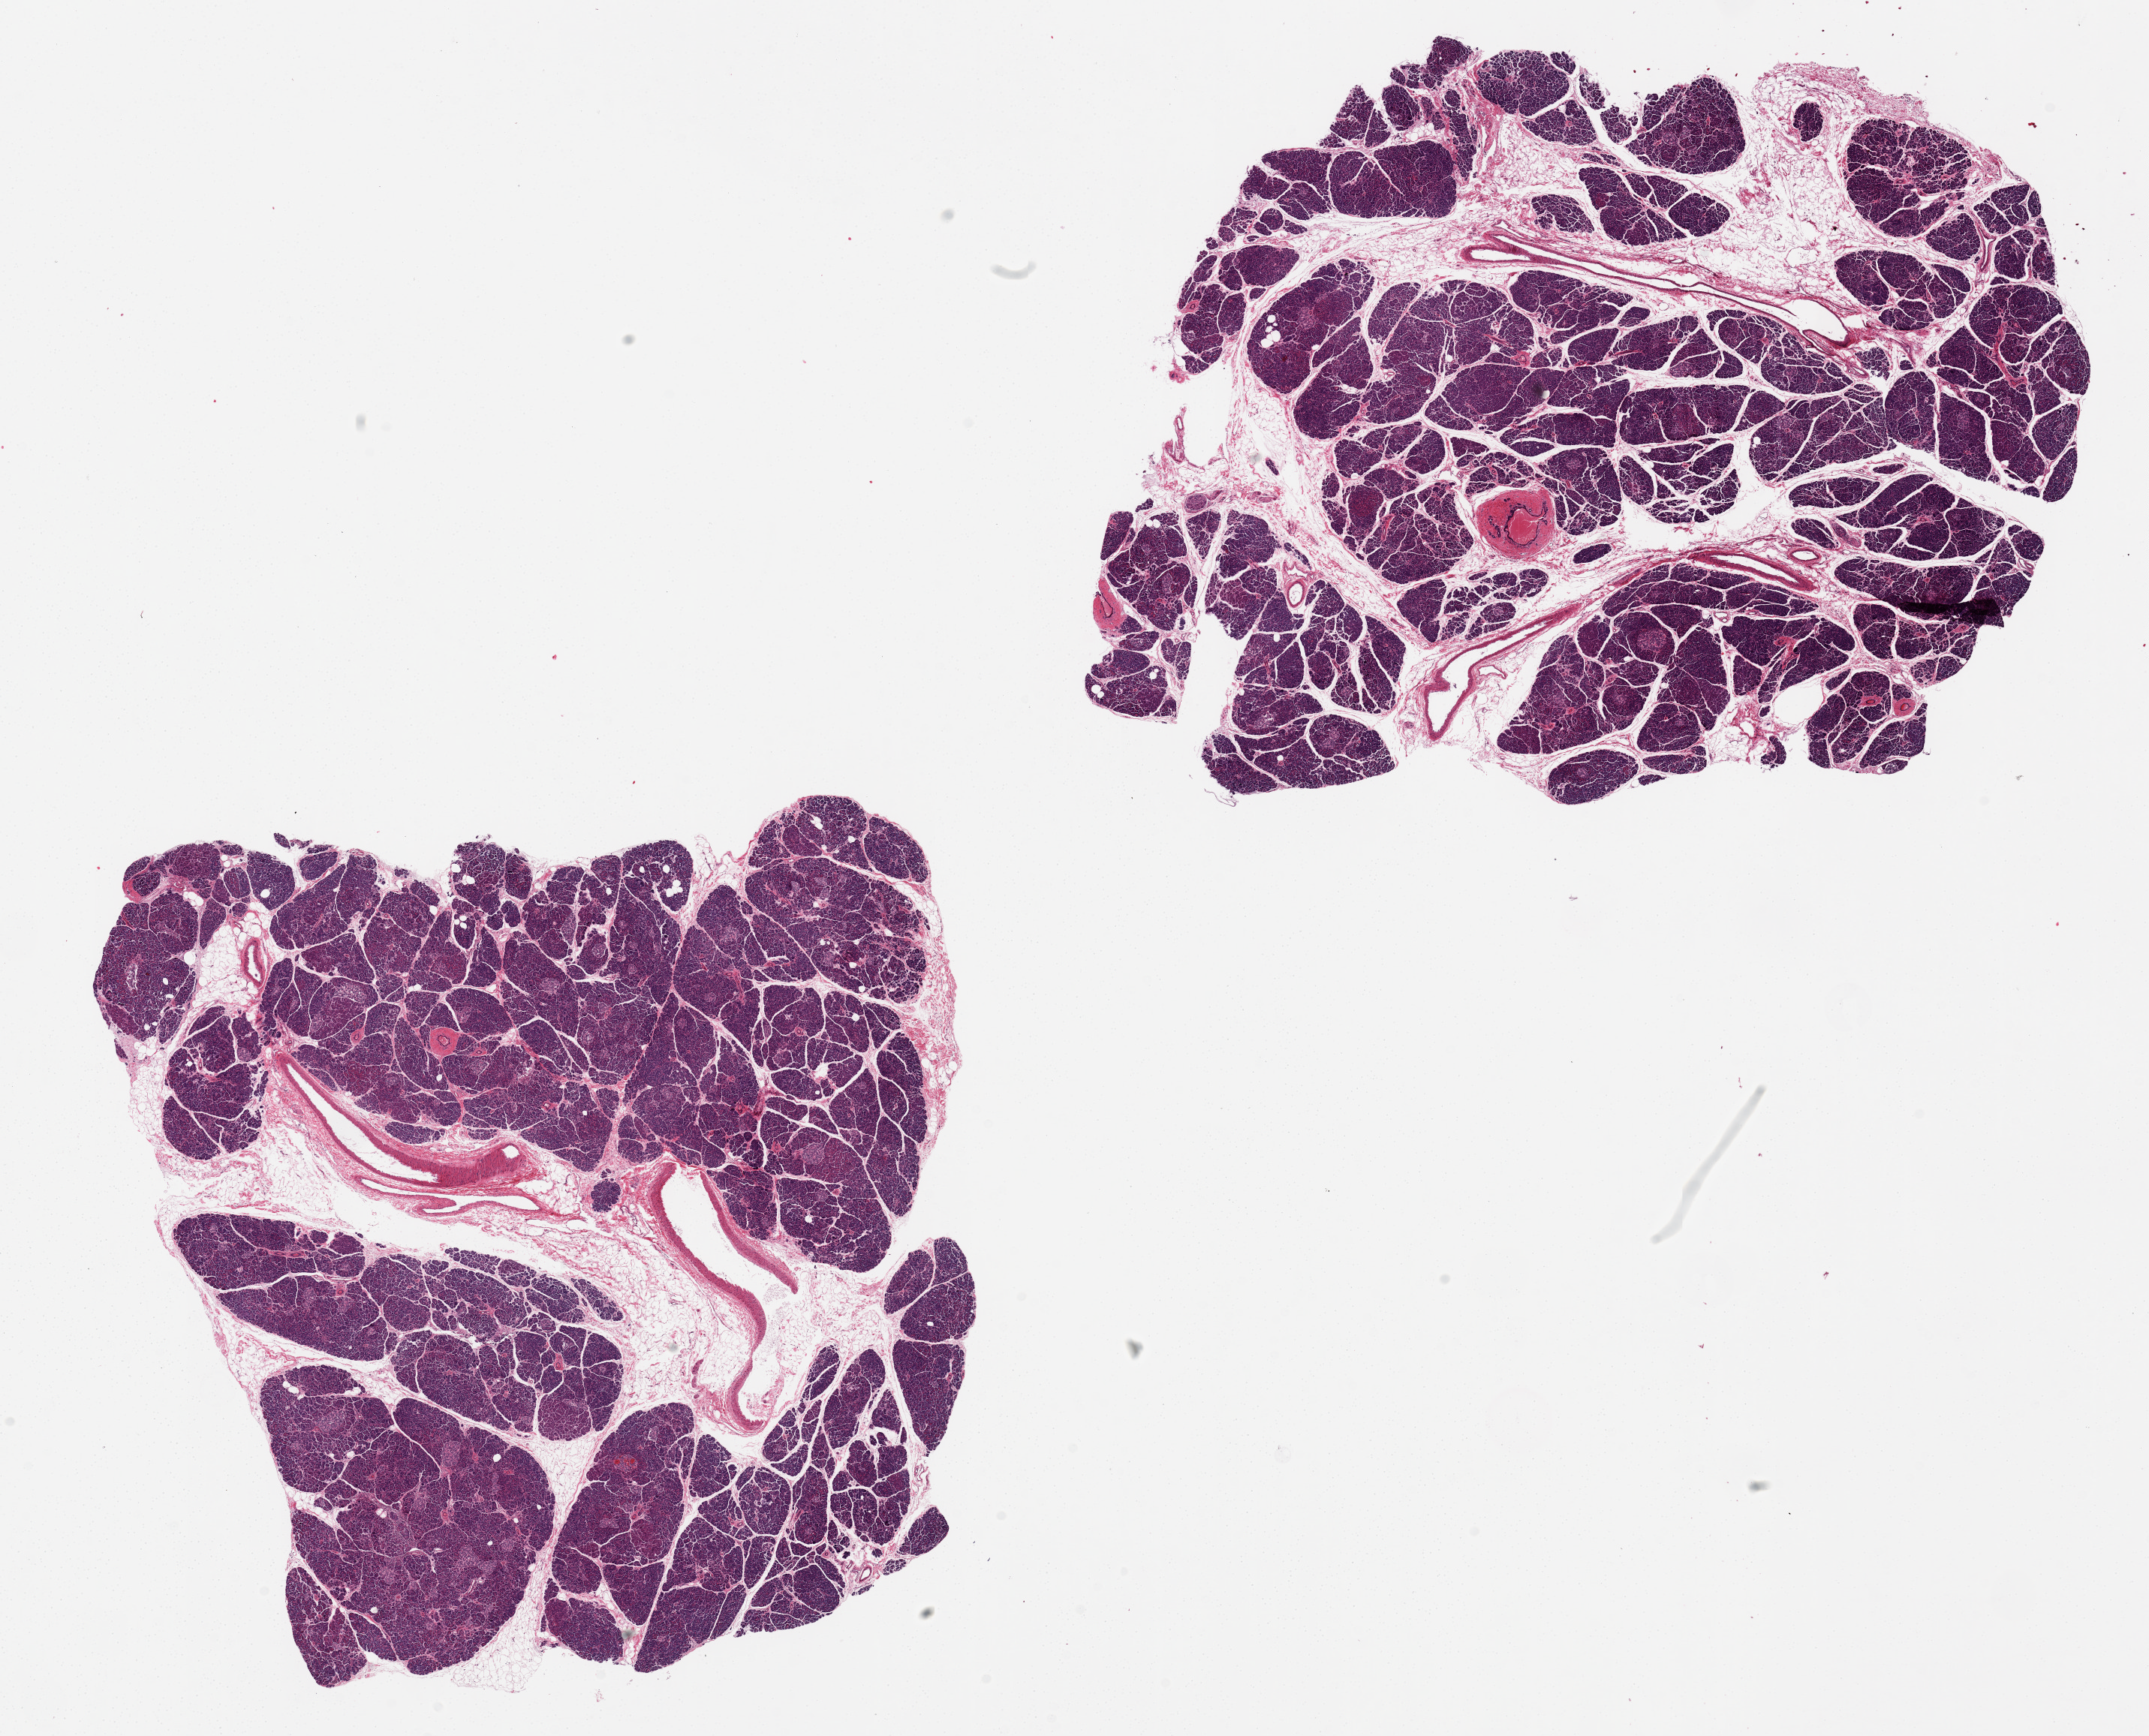
Whole-slide image, haematoxylin and eosin stain — whole scanned area (about 22.6 x 18.3 mm, slide scanned at 20x) shown as a low-resolution overview, PAXgene-fixed paraffin-embedded (PFPE) section, sampled site (target tissue): pancreas, tissue donor sample.
- review note (as recorded): 2 pieces; 10-20% internal fibroadipose; focal hemorrhages in ducts